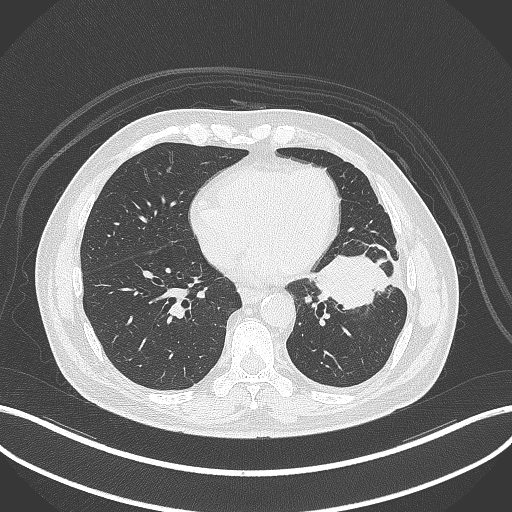
Chest CT, one axial slice. Slice 135 of 230 in the series (ordered by position). Lung window (W 1500 / L -600 HU). 512 × 512 image matrix, field of view 400 × 400 mm. Patient: male, 68 years. Case-level facts recorded for this patient, not image findings: clinical TNM (as recorded): T2b N0 M0.
Structures marked on this image (rectangle marked by the reading radiologist):
- lung tumour (recorded histology: squamous cell carcinoma): bounding box [x1, y1, x2, y2] px = [310, 251, 393, 311]